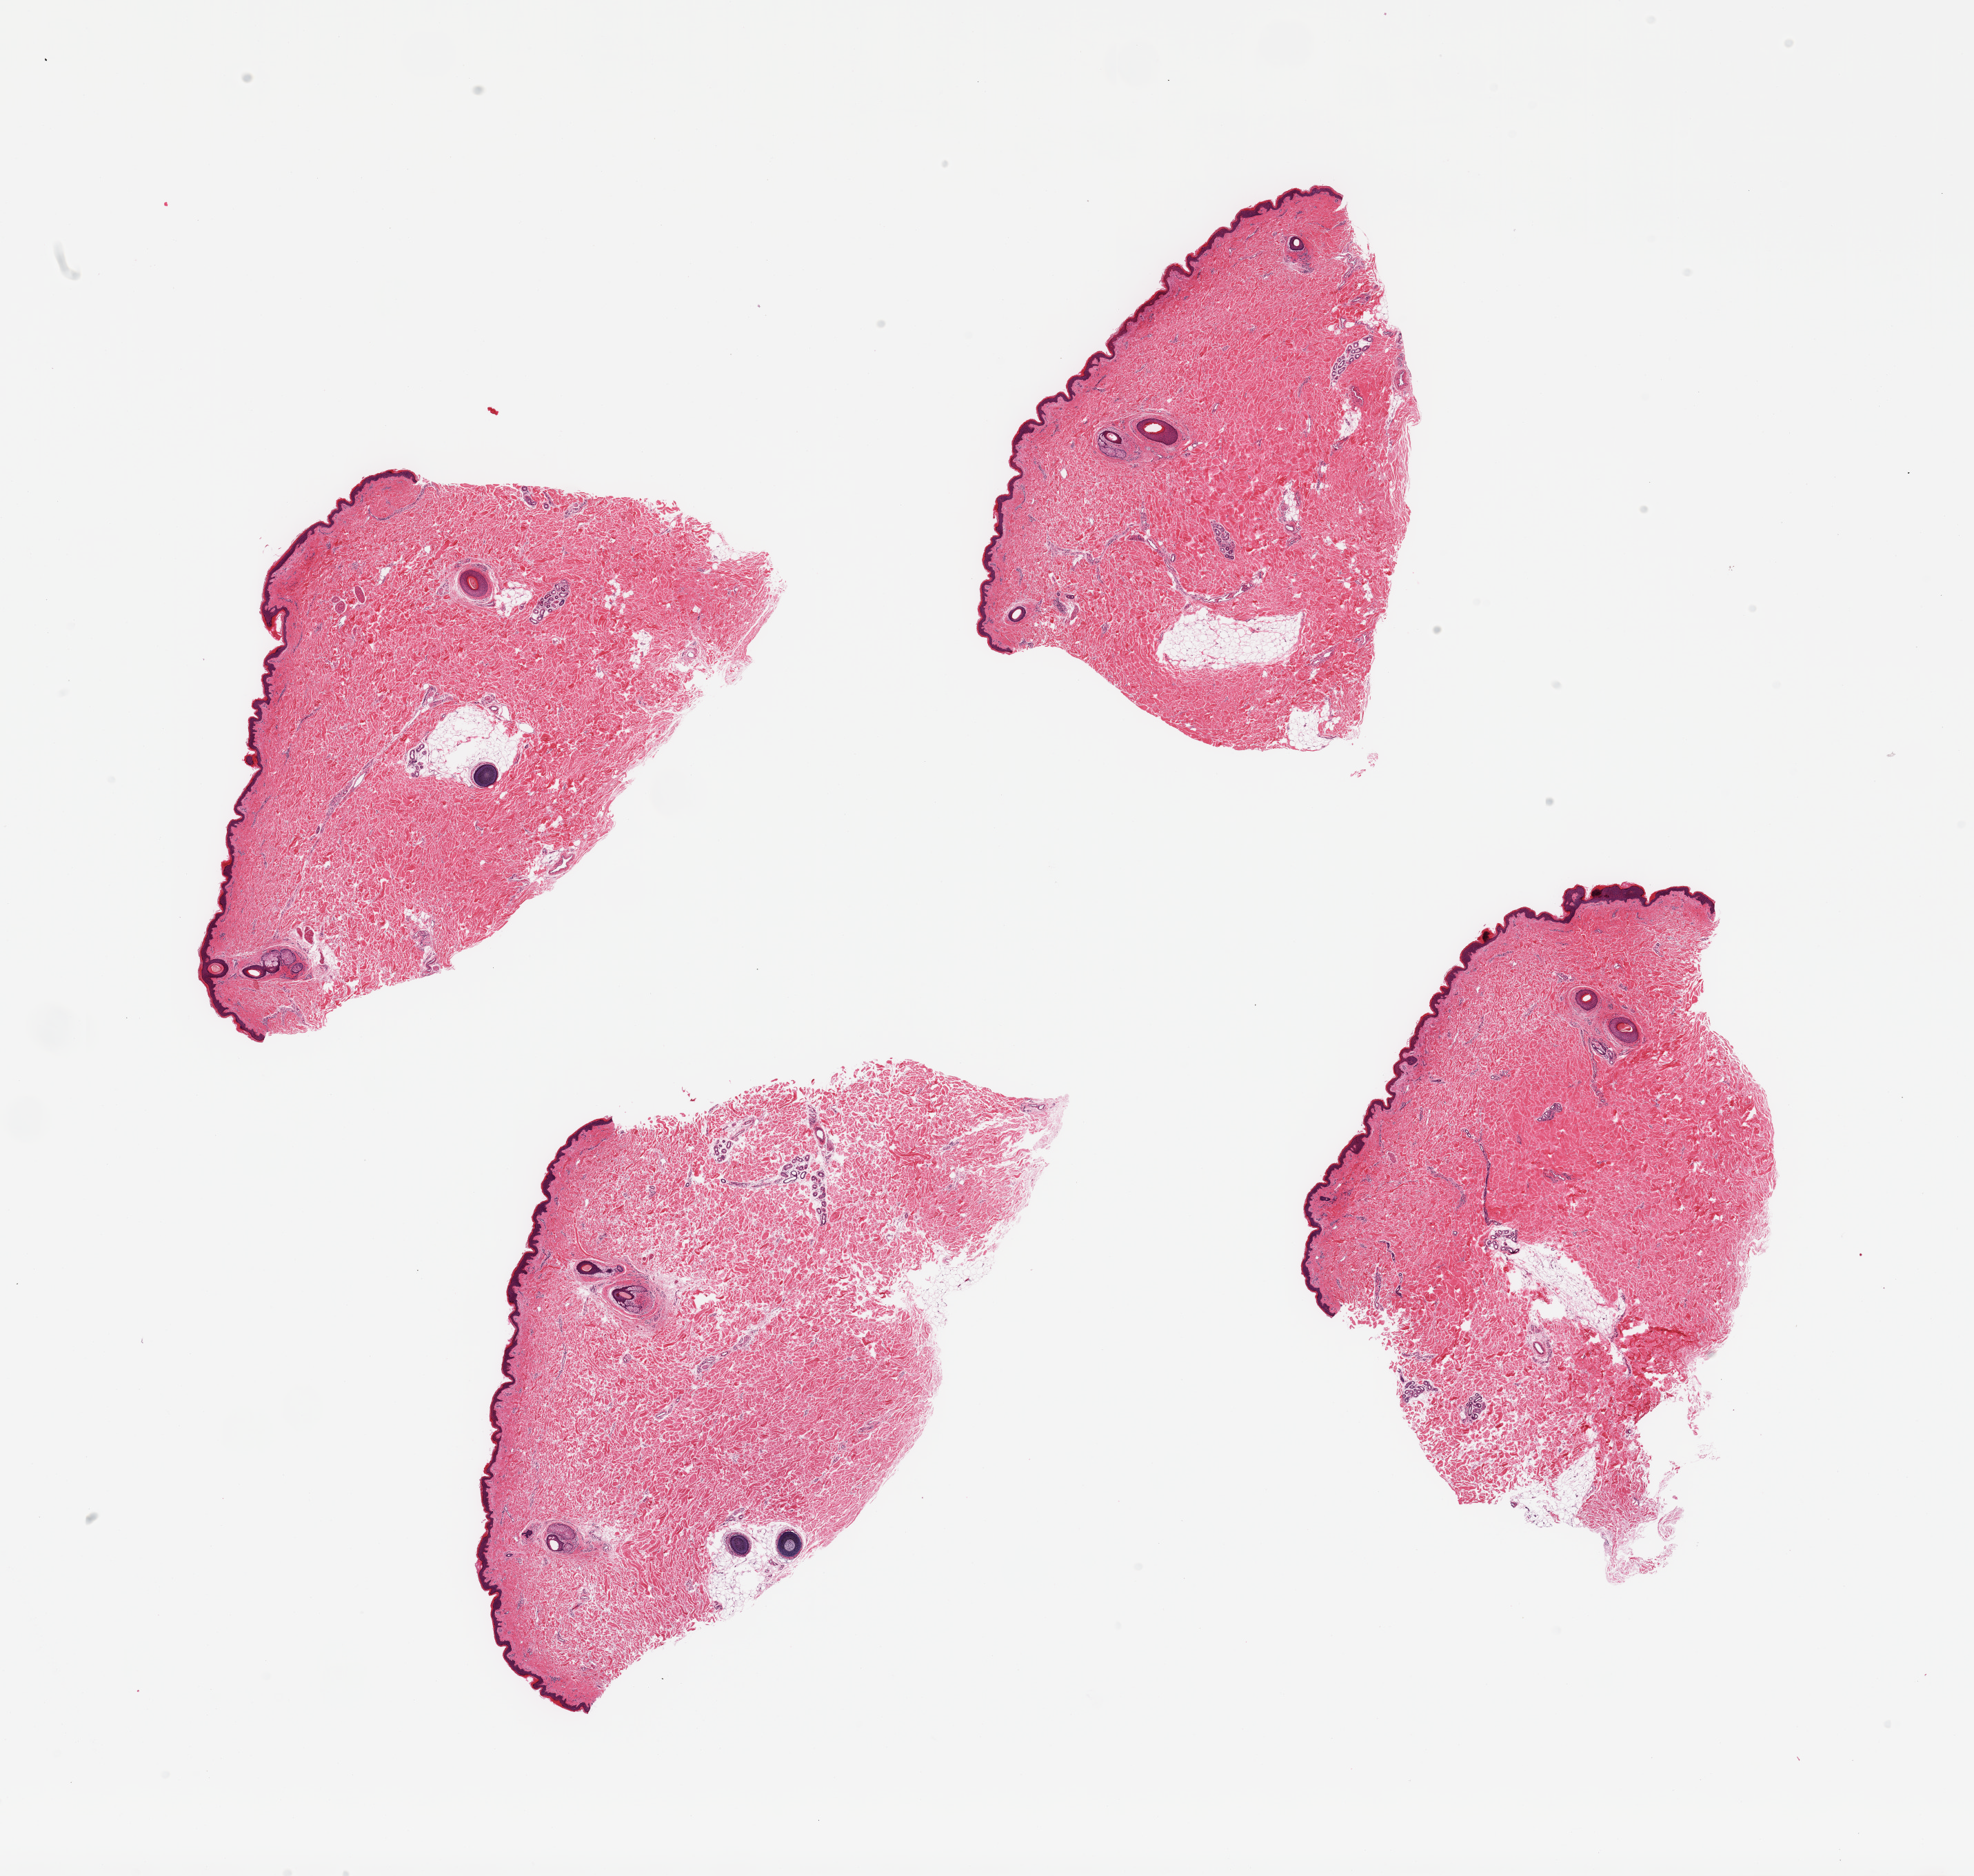
Hematoxylin and eosin (H&E) whole-slide image, brightfield — shown as a low-resolution overview of the whole scanned area (about 22.6 x 21.5 mm), PAXgene-fixed paraffin-embedded (PFPE) section, target tissue: skin of suprapubic region, donor tissue sample. Donor: male.
Reviewer comment on this tissue sample: 4 pieces; hair bearing skin and ~5% periadnexal (internal) fat.